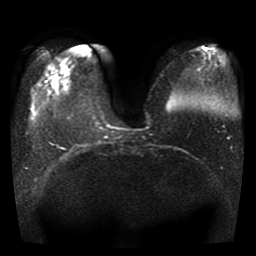
Breast MRI, one axial slice; position 11 of 41 along the scan axis; diffusion-weighted series; image 2 of 4 stored at this slice position (different b-values; order by instance number); 1.5 T; 5 mm slice thickness; 256 × 256 image matrix, field of view 330 × 330 mm. Female patient.
Structures marked on this image (manually delineated by an expert):
- tumour on diffusion-weighted imaging: bounding box <54,76,58,86> (left, top, right, bottom; pixels)